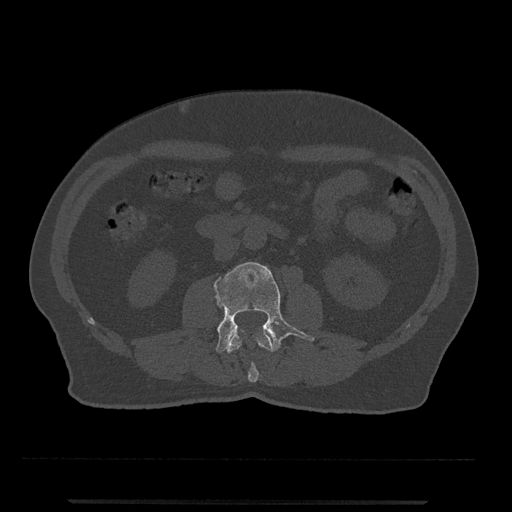
CT including the spine, one axial slice; slice 220 of 797 in the series (ordered by position); reconstruction kernel Br40s/3; bone window (W 1800 / L 400 HU); 0.5 mm slice thickness; 512 × 512 image matrix. Male patient, age 63 years. From the clinical record (not read from this slice): primary cancer: prostate.
Structures marked on this image (semi-automatic segmentation, software-assisted and operator-edited):
- L2 vertebra: box from (x=227, y=332) to (x=273, y=383) px
- L3 vertebra: (x=212, y=262)–(x=315, y=353)